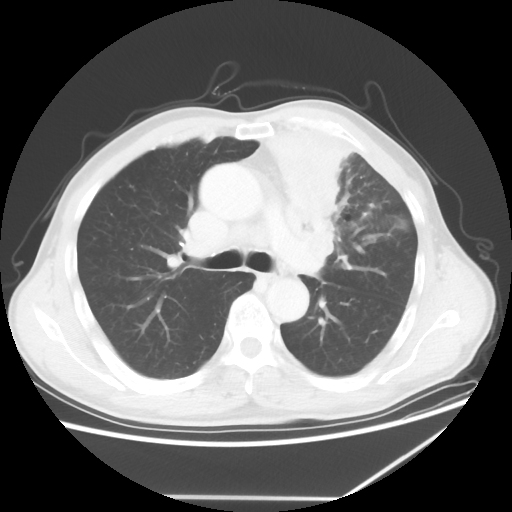
Chest CT, one axial slice. Slice 40 of 64 in the series (ordered by position). 100 kVp. Lung window (W 1500 / L -600 HU). 5 mm slice thickness. 512 × 512 image matrix, field of view 383 × 383 mm. Male patient, age 64 years. Case-level facts recorded for this patient, not image findings: clinical TNM (as recorded): T1c N1 M1.
Structures marked on this image (bounding box drawn by a radiologist):
- lung tumour (recorded histology: squamous cell carcinoma): bounding box [x1, y1, x2, y2] px = [262, 124, 351, 245]